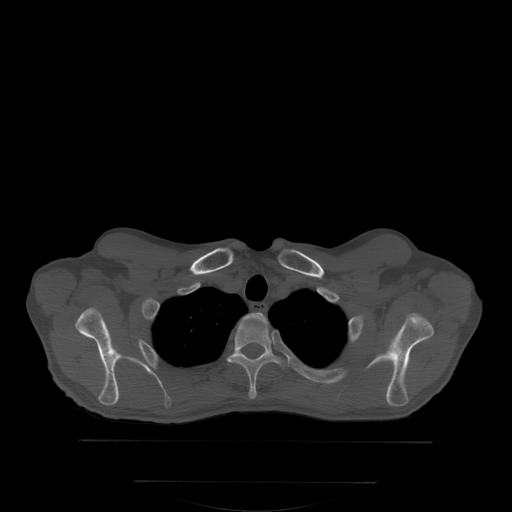
CT including the spine, one axial slice; position 278 of 350 along the scan axis; bone window (W 1800 / L 400 HU); 2.5 mm slice thickness; 512 × 512 image matrix, field of view 500 × 500 mm. Male patient, age 58 years. From the clinical record (not read from this slice): primary cancer: prostate.
Structures marked on this image (semi-automatic segmentation, software-assisted and operator-edited):
- T1 vertebra: bounding box (x1, y1, x2, y2) in pixels: (249, 313, 260, 317)
- T2 vertebra: (231, 314, 303, 398)
- T3 vertebra: (226, 350, 303, 368)